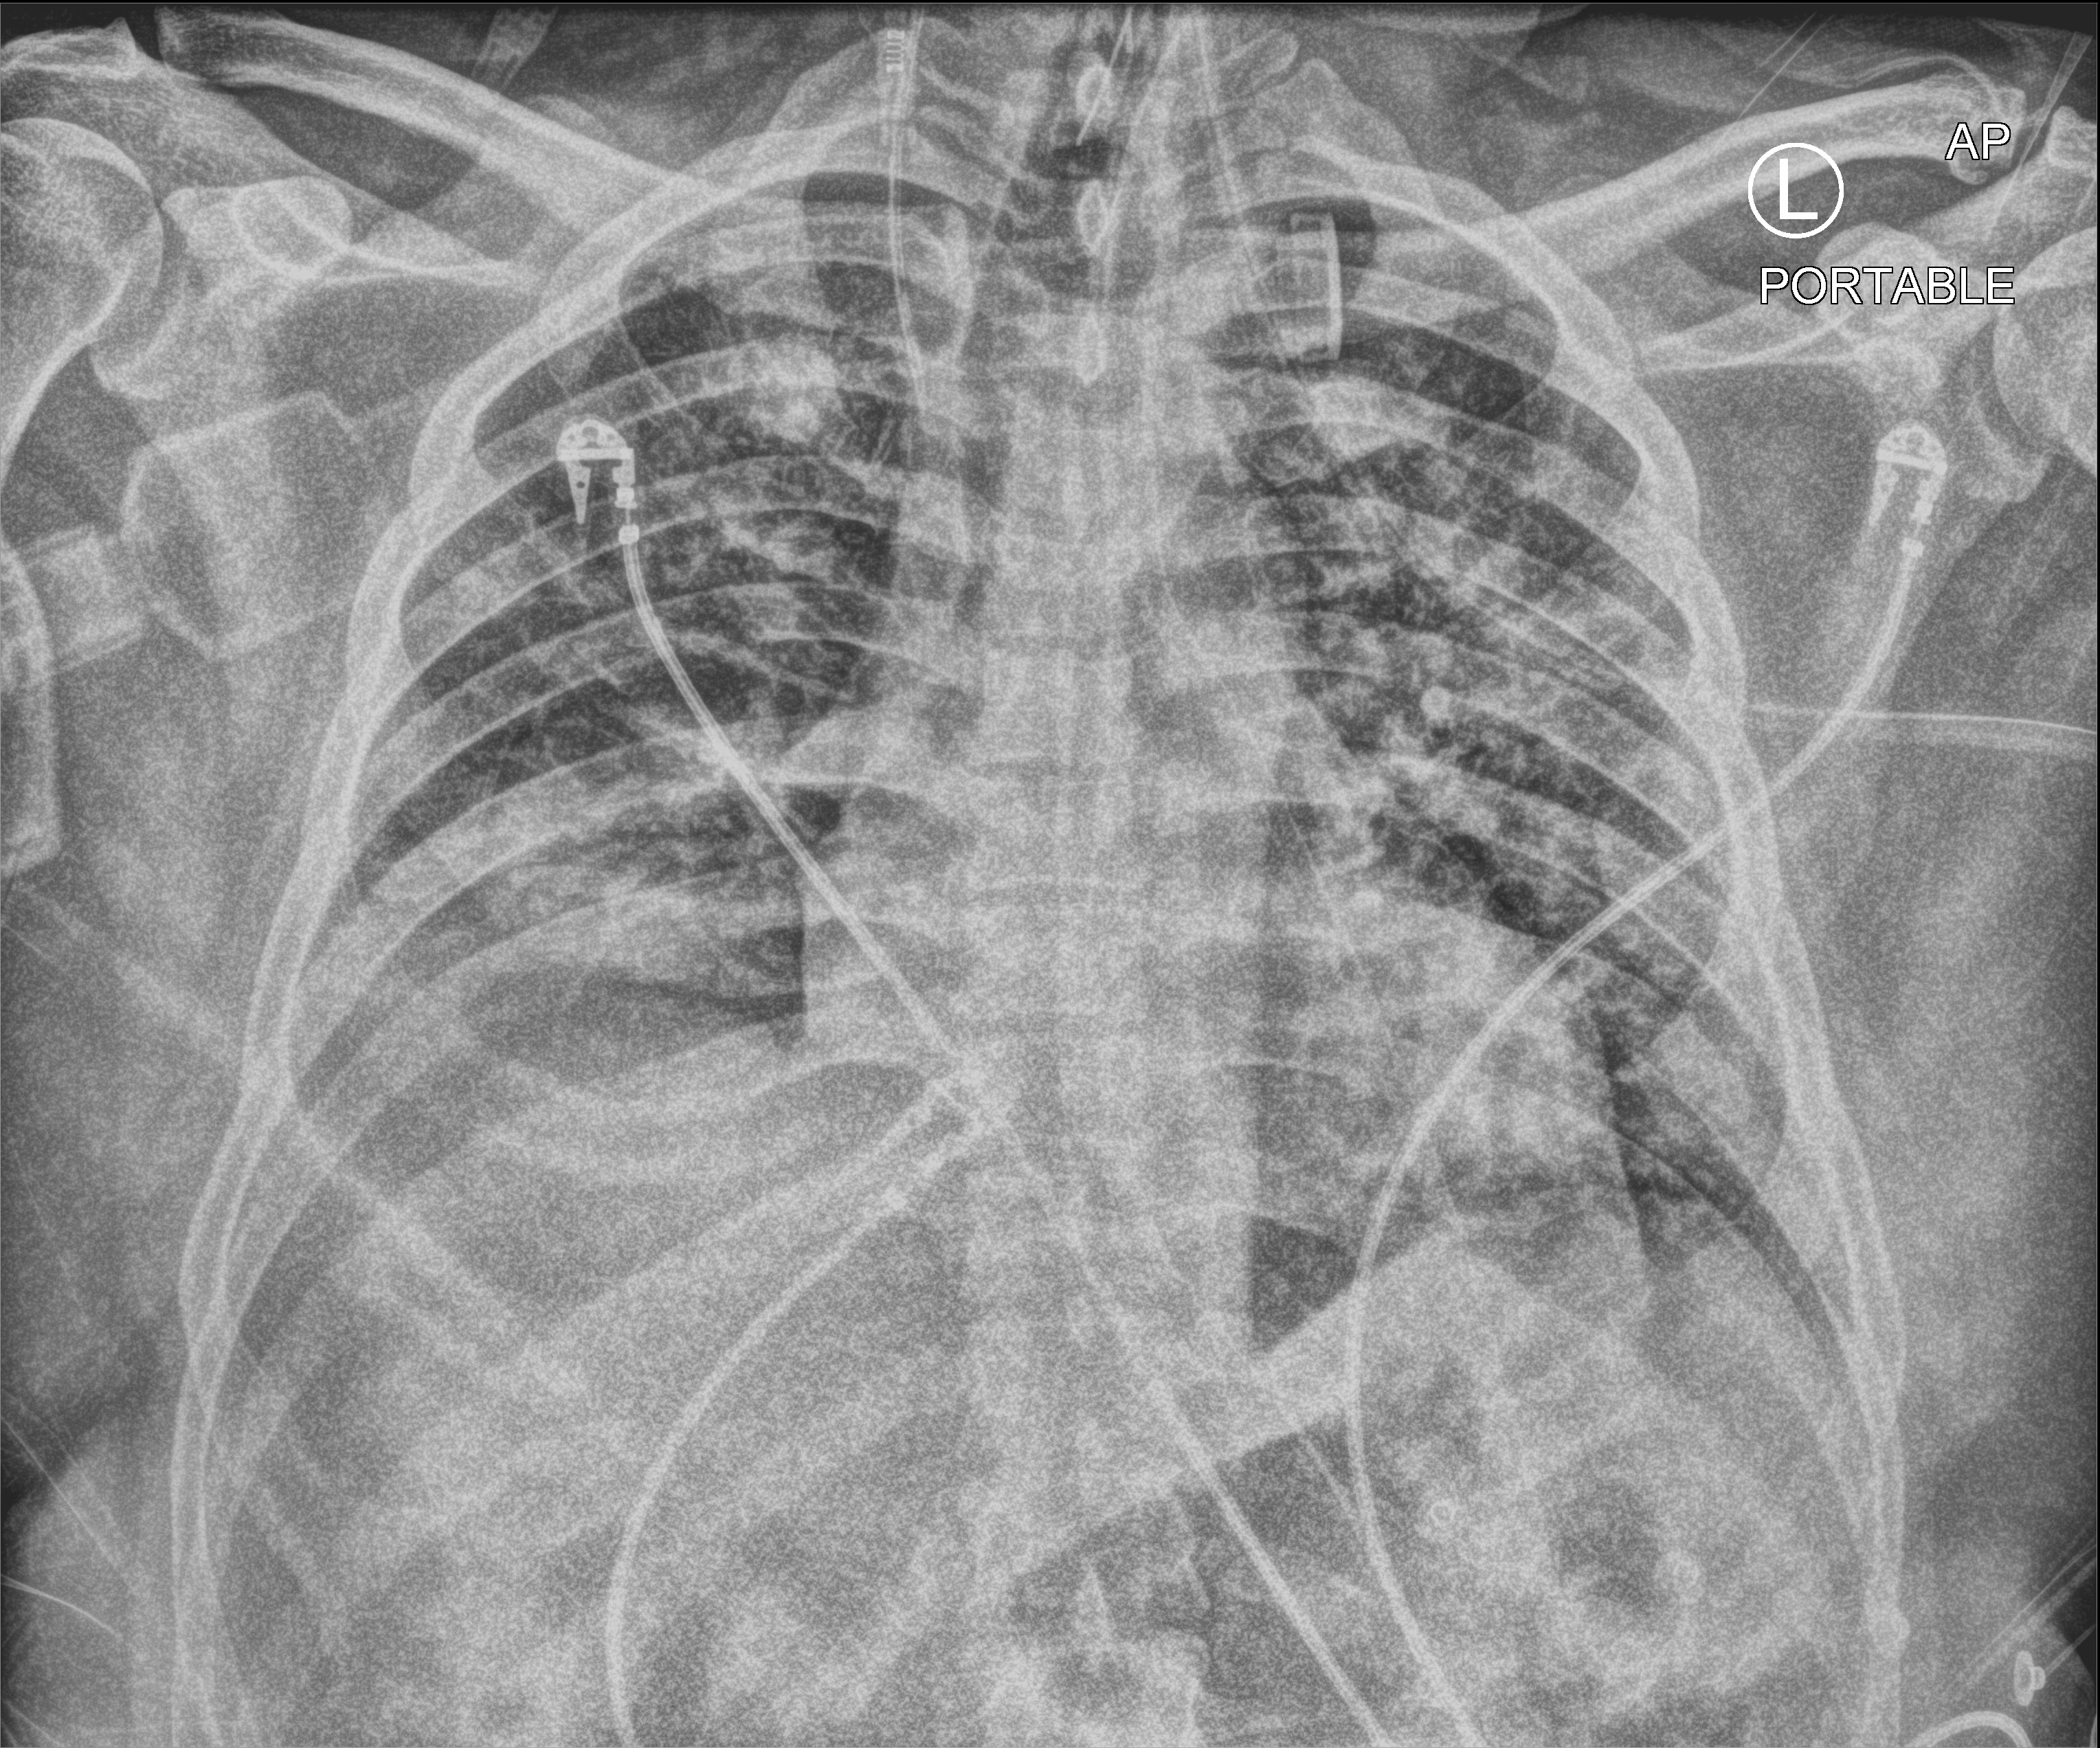
Chest X-ray (portable); anteroposterior (AP) projection. Patient hospitalised with COVID-19; male, aged 18–59 years.
Hospital-stay facts (about this admission, not read from this image; timing relative to this image not recorded): mechanically ventilated during this hospital stay: yes.